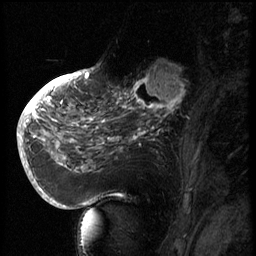
Breast MRI (dynamic contrast-enhanced), one sagittal slice; position 26 of 66 along the scan axis; 3 images stored at this slice position (order not interpretable as contrast timing); 1.5 T; TE 4.2 ms, TR 8.9 ms; 2.5 mm slice thickness; 256 × 256 image matrix, field of view 200 × 200 mm. Female patient, age 56 years. From the clinical record (not read from this slice): setting: breast cancer imaged before/during neoadjuvant chemotherapy.
Structures marked on this image (semi-automatically segmented with operator editing):
- analysis volume of interest (the breast-tissue region the enhancement analysis was run in; not a lesion): bounding box (x1, y1, x2, y2) in pixels: (129, 62, 194, 127)
- tumour enhancement mask (voxels above the 140 % enhancement threshold inside the analysis volume of interest): (129, 65, 187, 125)